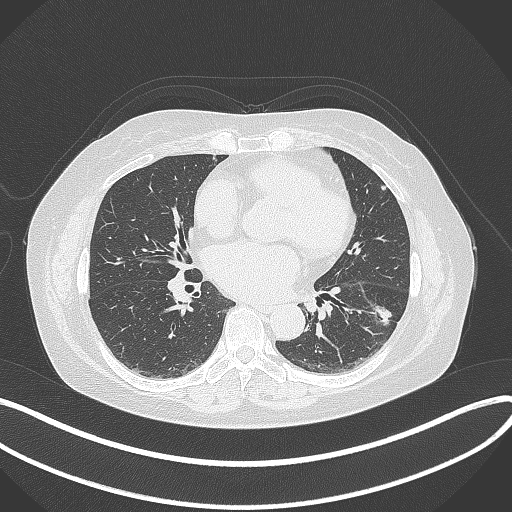
Chest CT, one axial slice; slice 167 of 373 in the series (ordered by position); reconstruction kernel B70f; 120 kVp; lung window (W 1500 / L -600 HU); 1 mm slice thickness; 512 × 512 image matrix, field of view 400 × 400 mm. Patient: female, 67 years. From the clinical record (not read from this slice): clinical TNM (as recorded): T1c N0 M0.
Annotated regions visible in this slice (rectangle marked by the reading radiologist):
- lung tumour (recorded histology: adenocarcinoma): bounding box <361,296,397,334> (left, top, right, bottom; pixels)